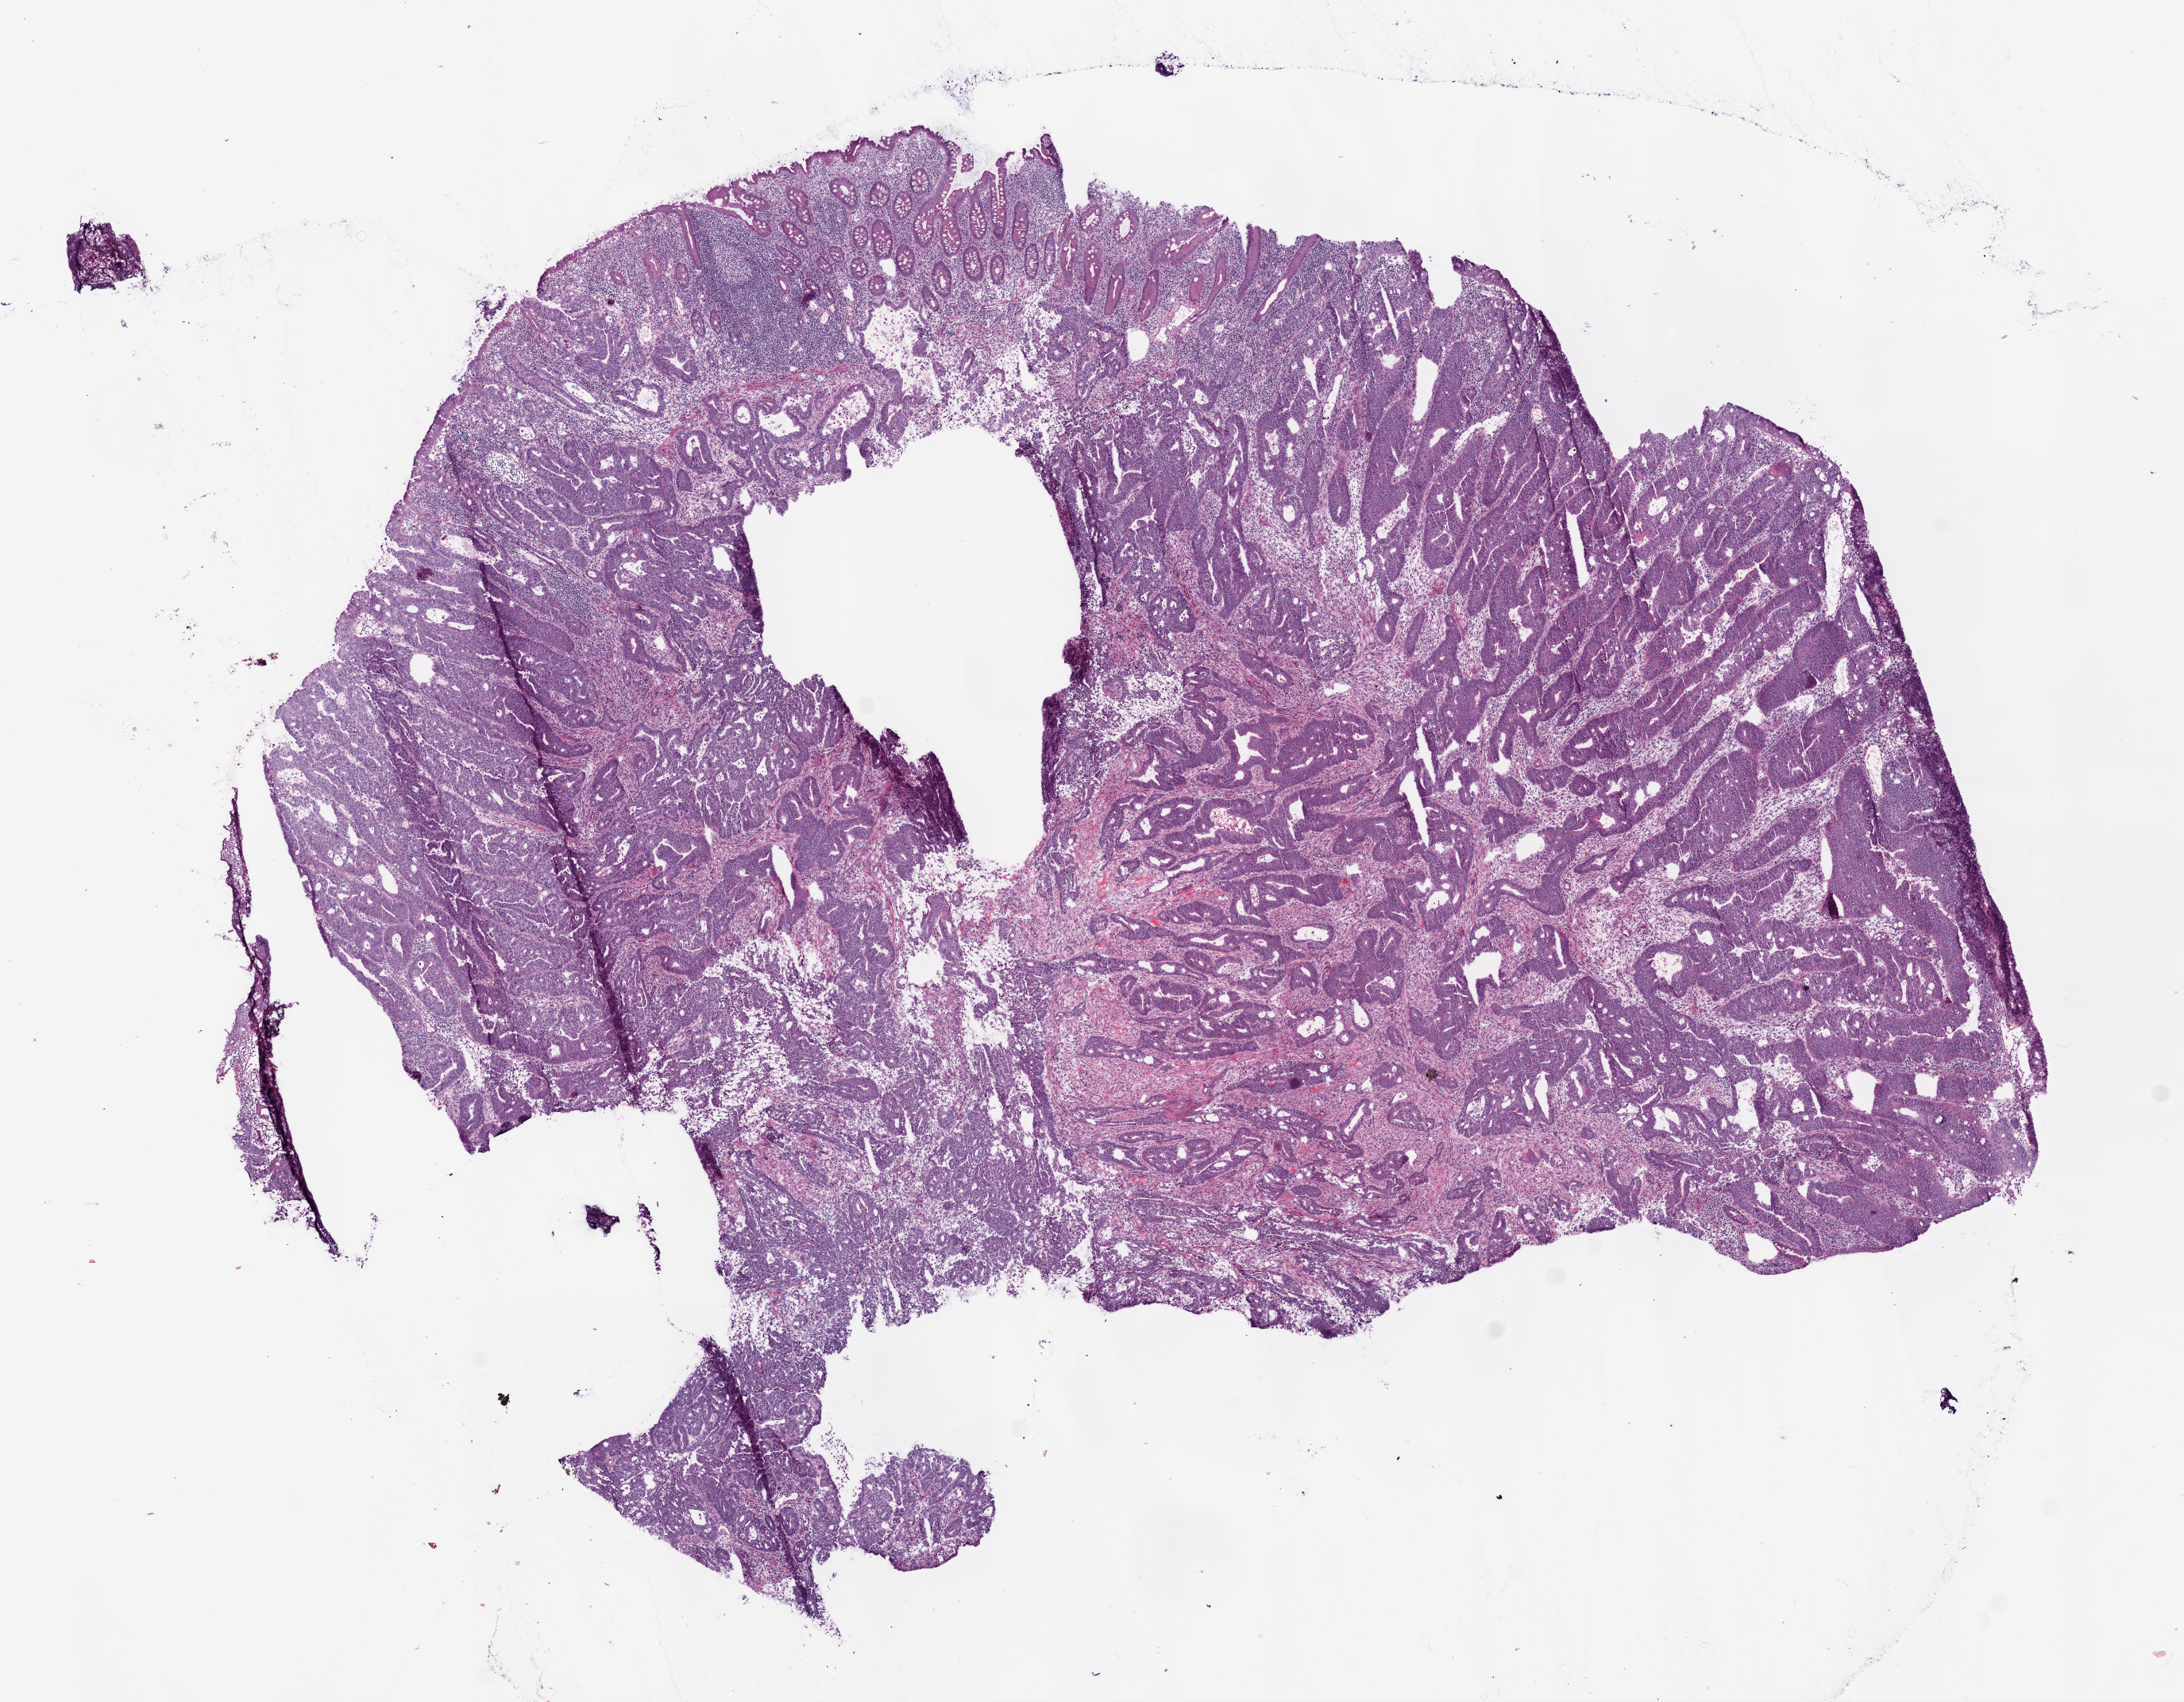
Whole-slide histology image, H&E-stained — whole scanned area (about 11.0 x 8.6 mm, acquisition: 20x scan) shown as a low-resolution overview. Frozen section from the bottom of the tissue portion. Colon, primary tumour sample. Female patient; age at initial diagnosis 71 years. Pathologist review of this section (percent, as recorded): tumour cells 77%, tumour nuclei 85%, normal cells 3%, stromal cells 20%, necrosis 0%.
AJCC pathologic stage: IIIC (6th edition). Diagnosis: Adenocarcinoma, NOS. TNM: T3 N2 M0. Lymph nodes positive (case pathology): 4 of 23 examined.